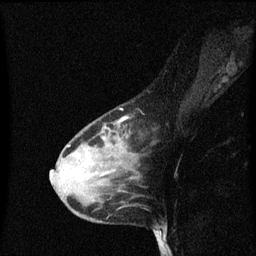
Breast MRI (dynamic contrast-enhanced), one sagittal slice. Slice 42 of 60 in the series (ordered by position). Dynamic contrast-enhanced series, image 2 of 3 at this slice position (ordered by acquisition). 1.5 T. TE 4.2 ms, TR 8.4 ms. 2 mm slice thickness. 256 × 256 image matrix, field of view 200 × 200 mm. Female patient, age 38 years. From the clinical record (not read from this slice): setting: breast cancer imaged before/during neoadjuvant chemotherapy; receptor status: HR-positive, HER2-negative.
Structures marked on this image (semi-automatic segmentation, software-assisted and operator-edited):
- analysis volume of interest (the breast-tissue region the enhancement analysis was run in; not a lesion): box from (x=50, y=112) to (x=139, y=205) px
- tumour enhancement mask (voxels above the 70 % enhancement threshold inside the analysis volume of interest): (x=62, y=118)–(x=127, y=177)